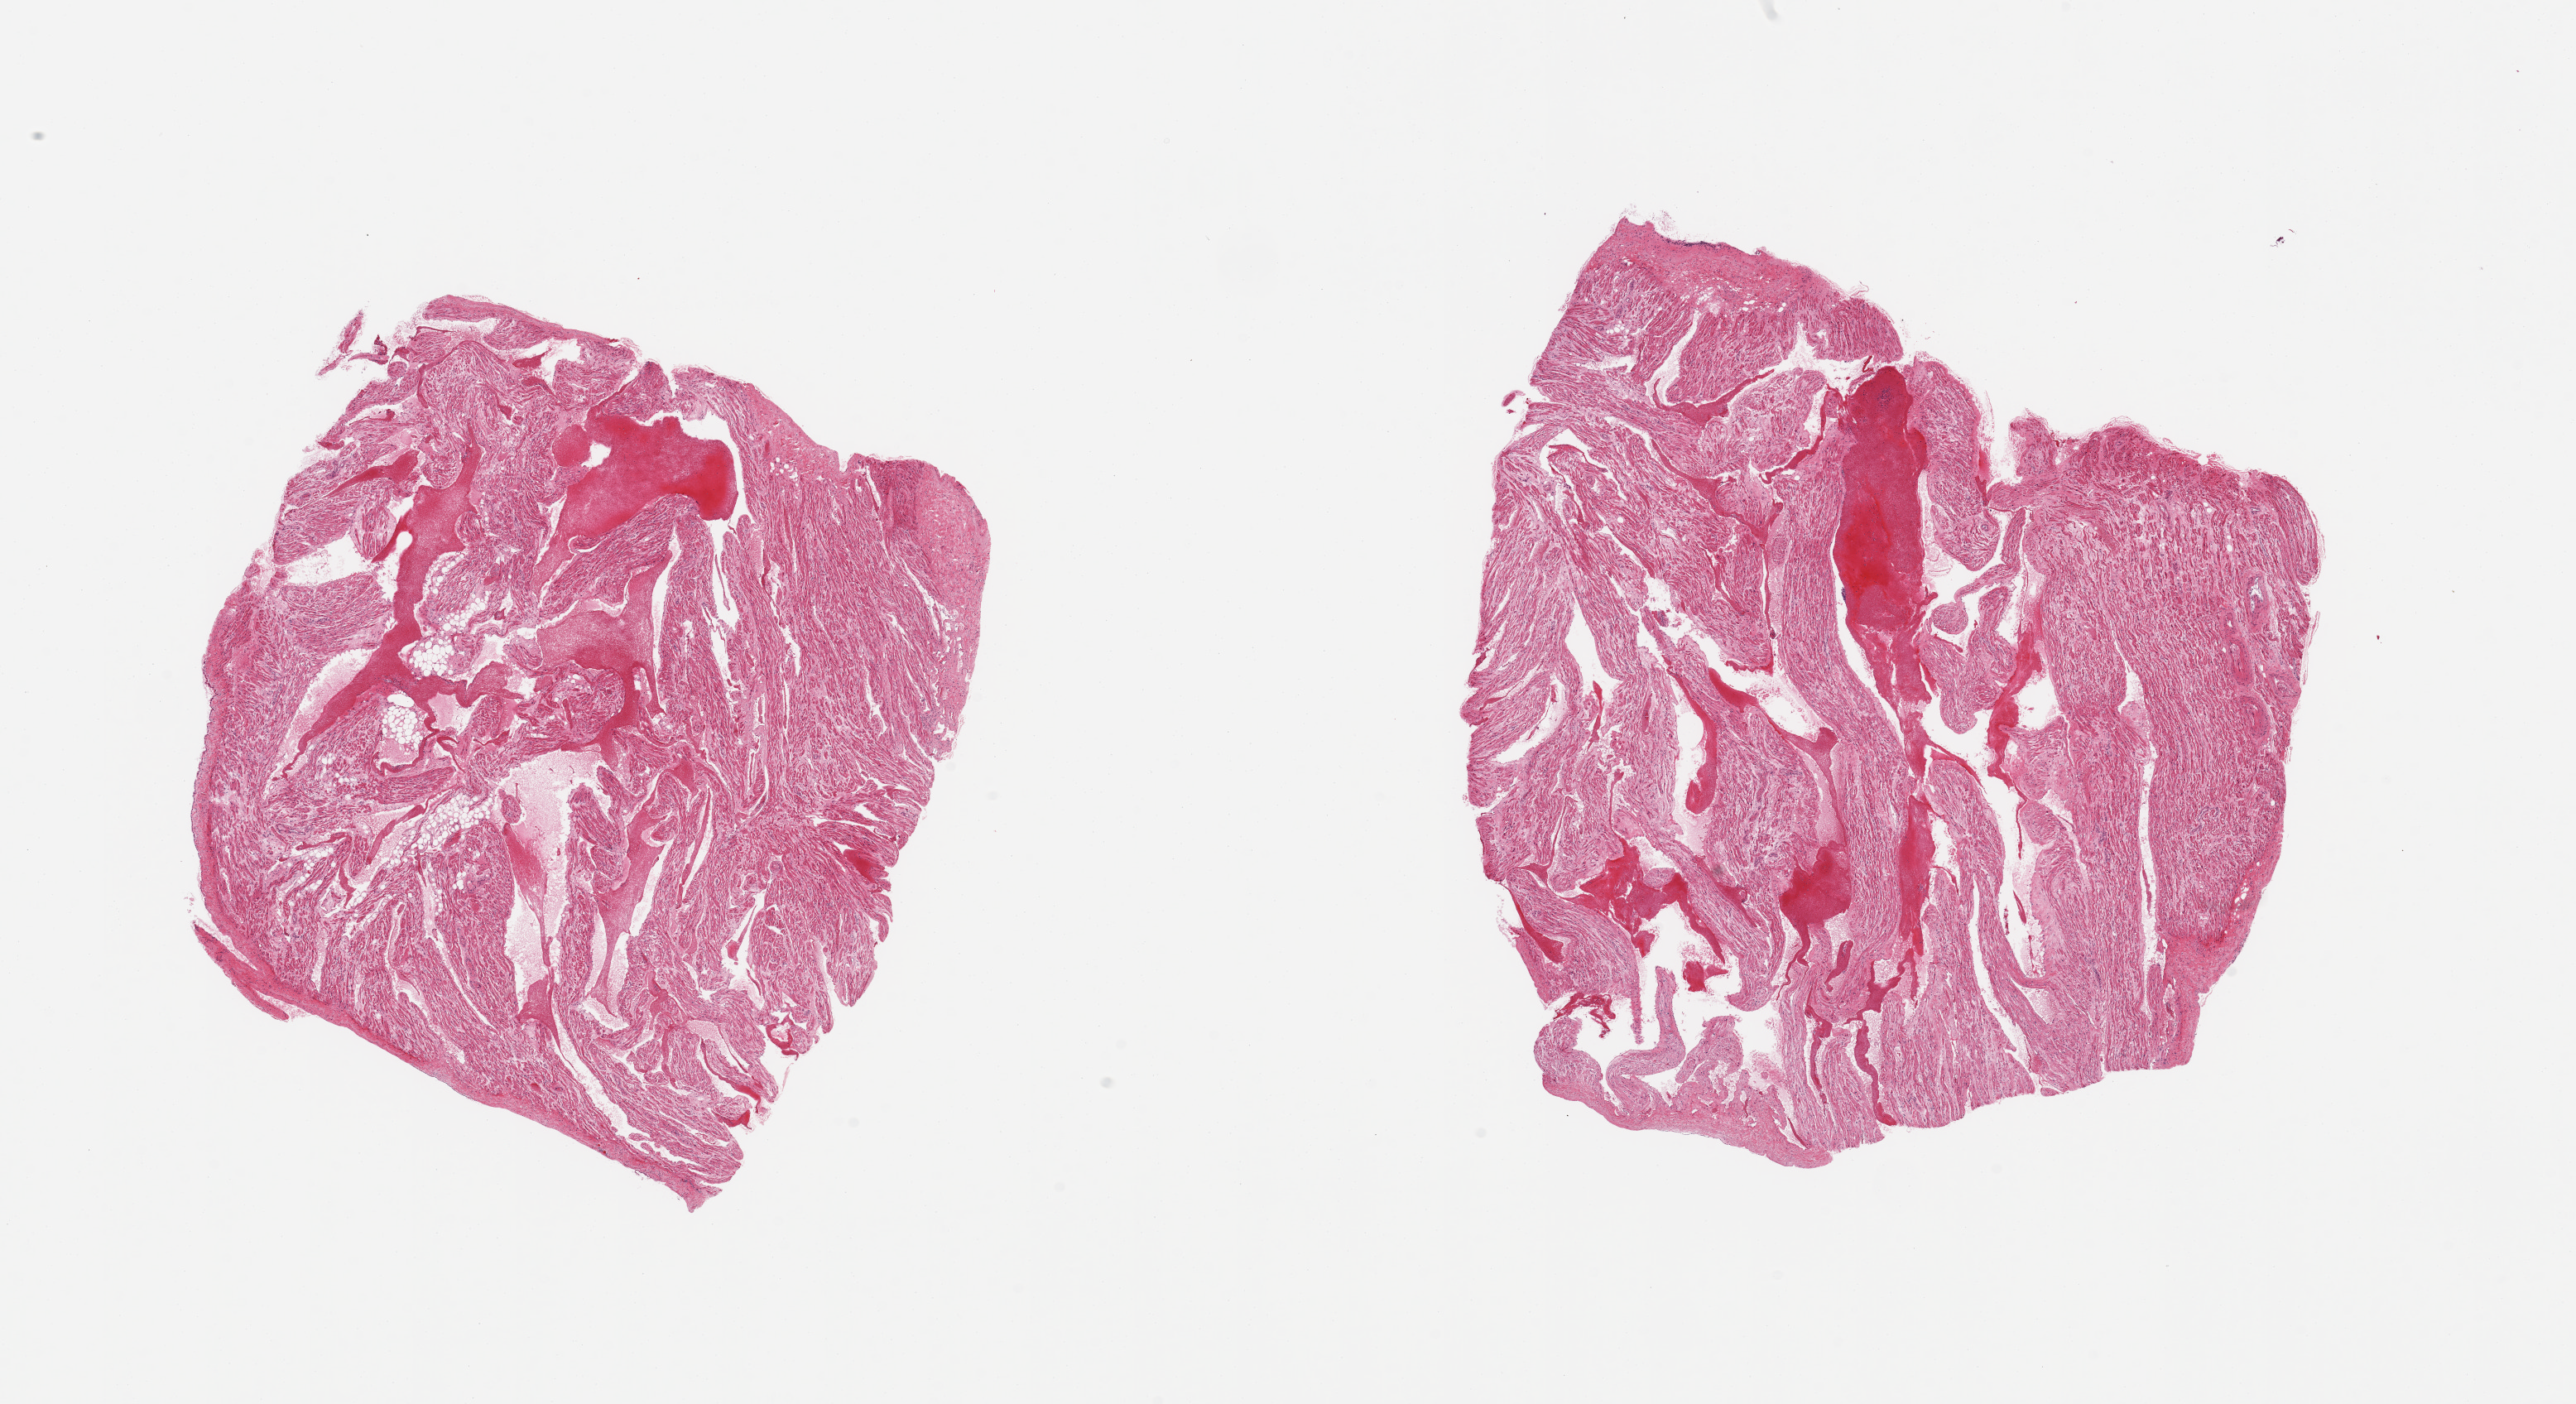
Digitized hematoxylin and eosin (H&E)-stained section — low-resolution overview of the scanned area, about 24.6 x 13.4 mm (slide scanned at 20x), PAXgene-fixed, paraffin-embedded tissue, section of auricular appendage (target tissue), donor tissue sample. Donor sex: female.
Pathologist's review note for this sample: 2 pieces; includes residual pooled blood/clot.